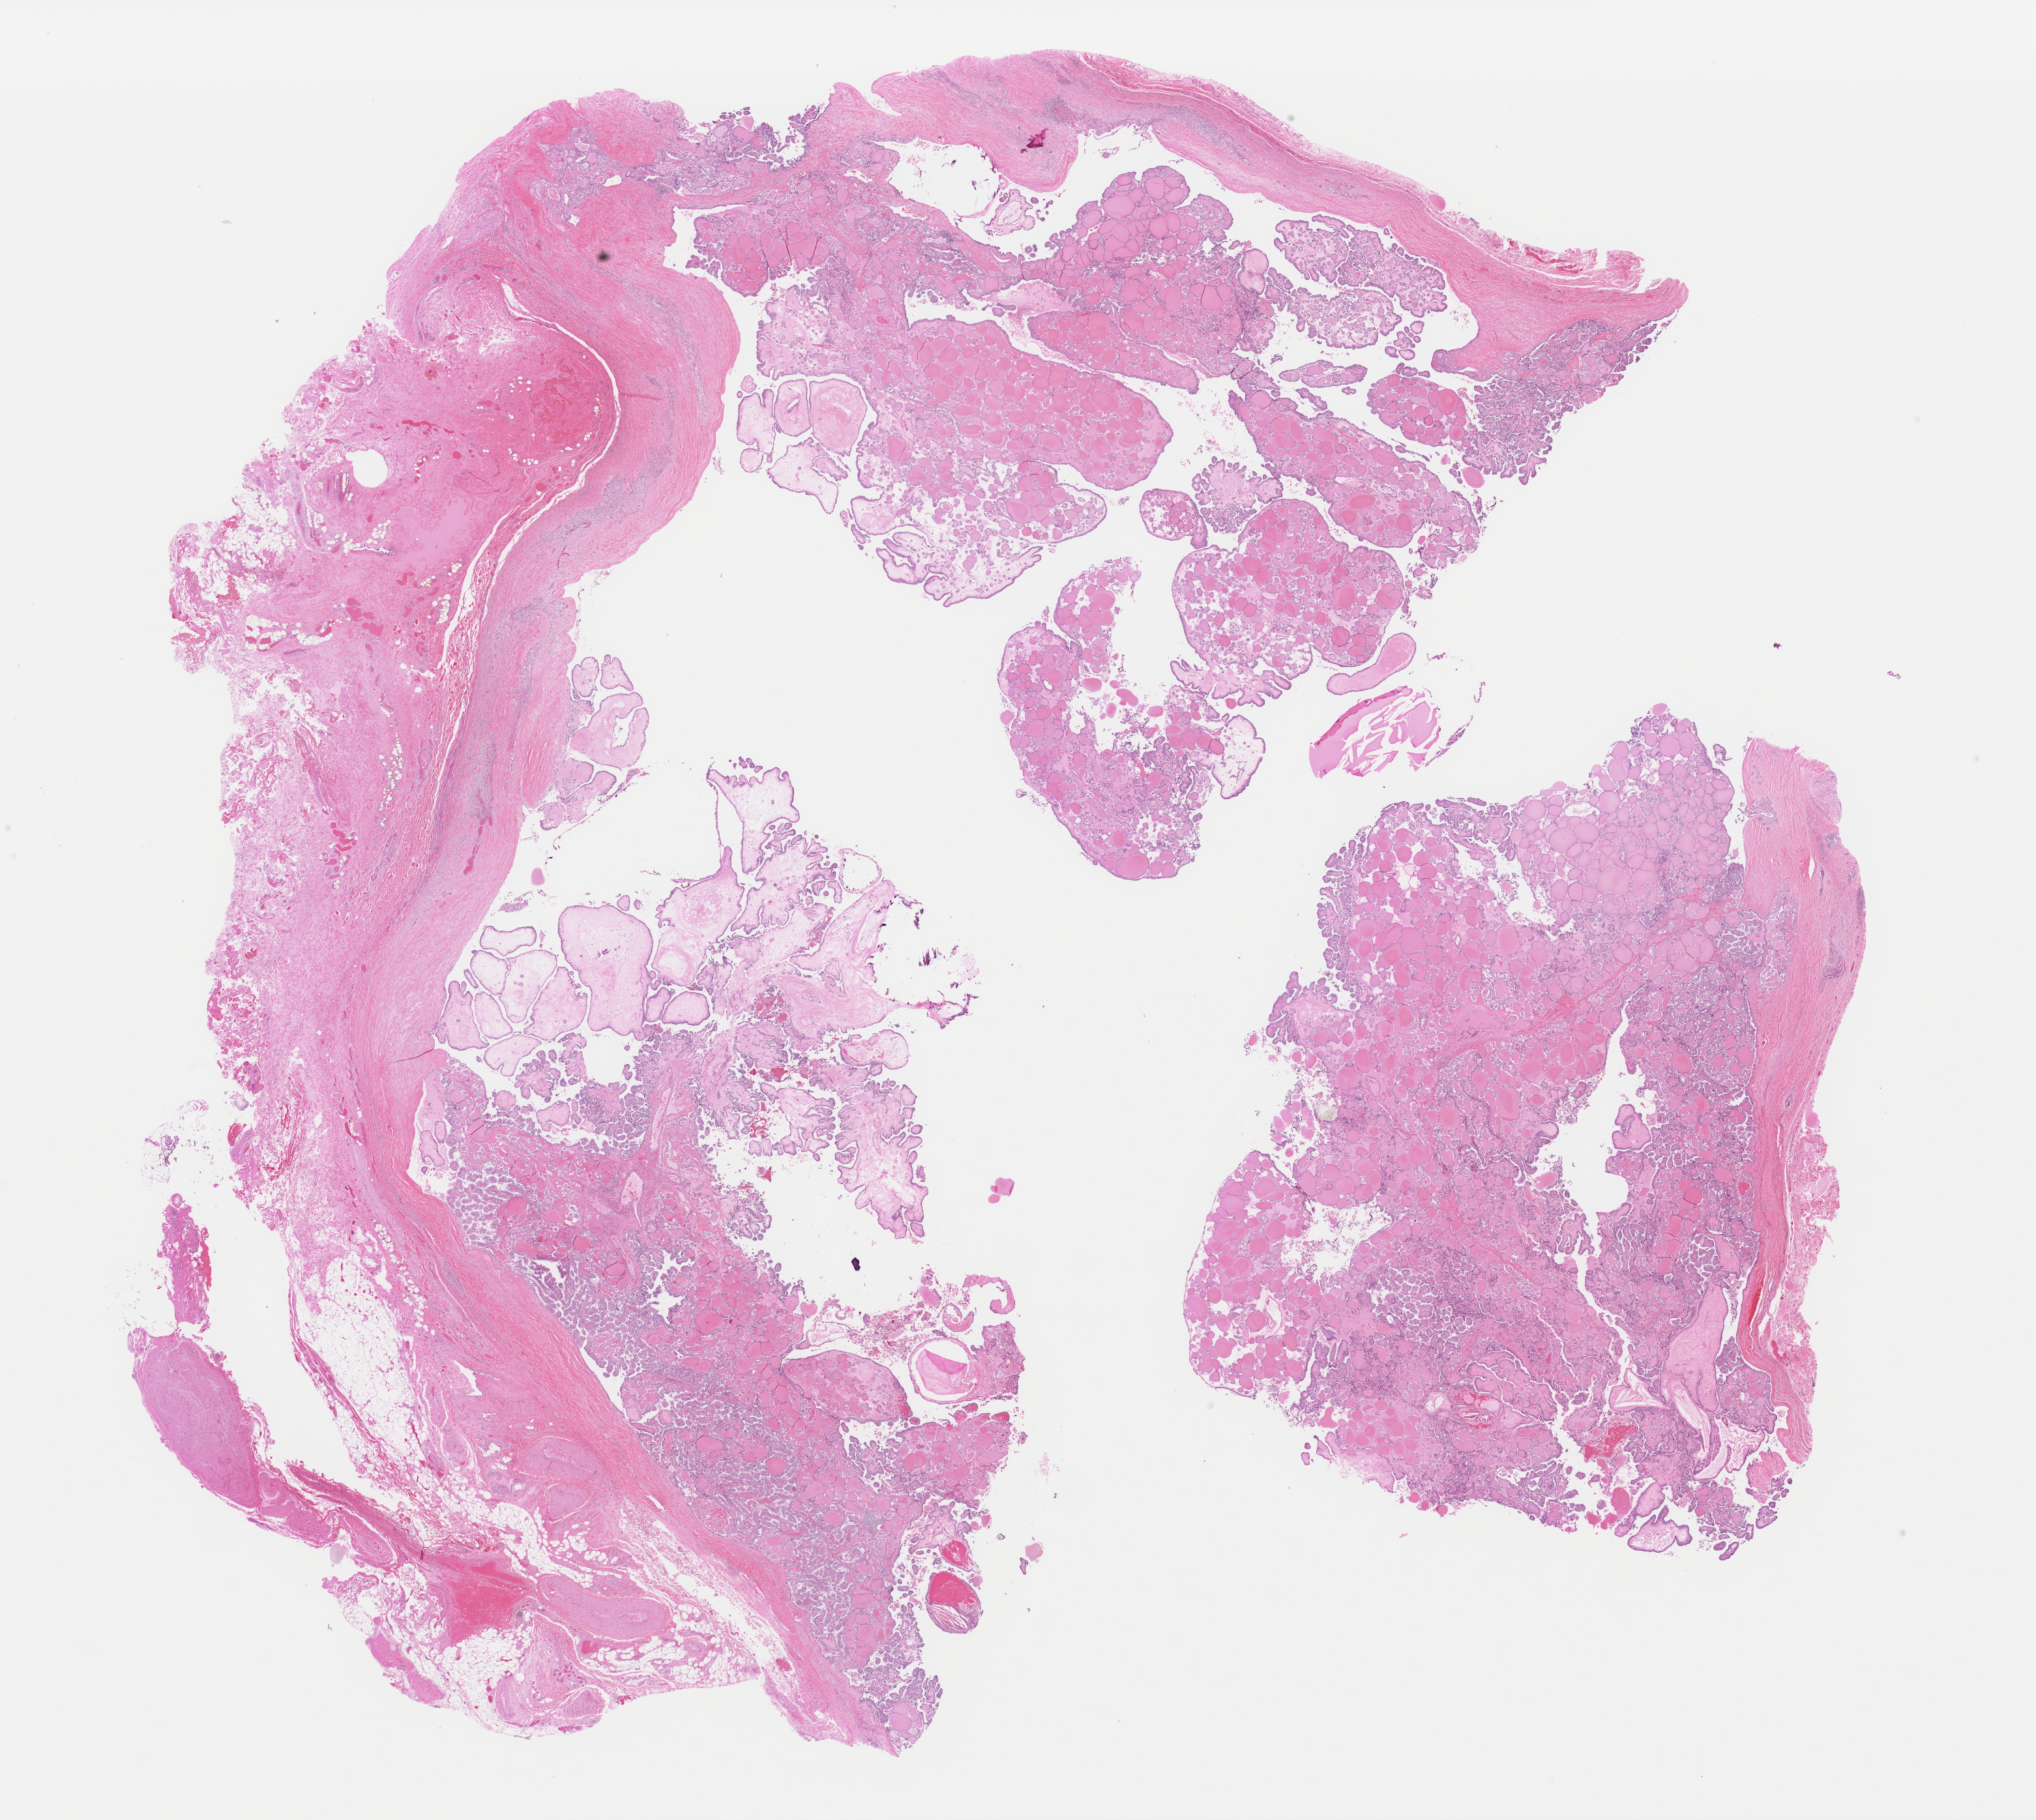
Digitized H&E-stained tissue section (whole slide), low-resolution overview of the scanned area, about 24.7 x 22.1 mm (slide scanned at 40x). Formalin-fixed paraffin-embedded (FFPE) diagnostic section. Sample: primary tumour, thyroid. Male patient; age at initial diagnosis 36 years.
• AJCC pathologic stage: I (6th edition)
• TNM: T2 N0 M0
• laterality: left
• pathologic diagnosis: Papillary adenocarcinoma, NOS (thyroid gland)